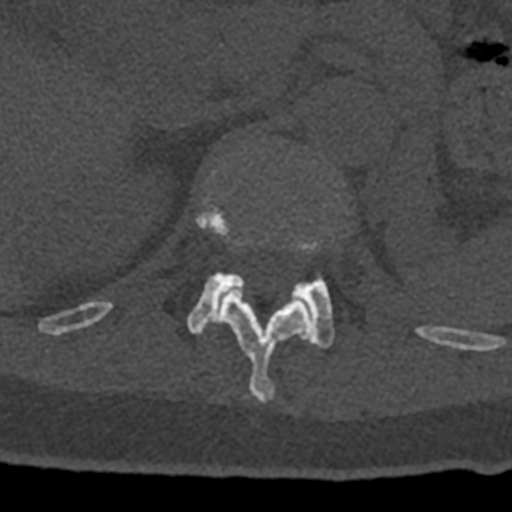
CT including the spine, one axial slice. Slice 466 of 797 in the series (ordered by position). Reconstruction kernel Br40s/3. Bone window (W 1800 / L 400 HU). 512 × 512 image matrix, field of view 160 × 160 mm. Patient: male, 74 years. From the clinical record (not read from this slice): primary cancer: renal.
Outlined on this slice (semi-automatic segmentation, software-assisted and operator-edited):
- L1 vertebra: box from (x=187, y=239) to (x=335, y=349) px
- T12 vertebra: (x=70, y=197)–(x=432, y=401)